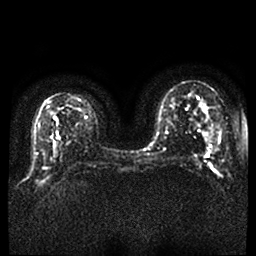
Breast MRI, one axial slice; position 23 of 52 along the scan axis; diffusion-weighted series; image 2 of 4 stored at this slice position (different b-values; order by instance number); 1.5 T; 4 mm slice thickness; 256 × 256 image matrix, field of view 340 × 340 mm. Female patient.
Annotated regions visible in this slice (outlined manually by an expert reader):
- tumour on diffusion-weighted imaging: bounding box [x1, y1, x2, y2] px = [210, 165, 214, 172]